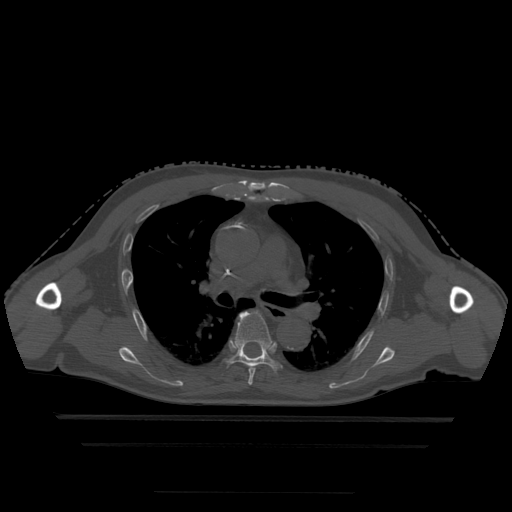
CT including the spine, one axial slice. Slice 321 of 522 in the series (ordered by position). Bone window (W 1800 / L 400 HU). 1.25 mm slice thickness. 512 × 512 image matrix, field of view 436 × 436 mm. Patient age 68 years. From the clinical record (not read from this slice): primary cancer: urothelial.
Annotated regions visible in this slice (semi-automatic segmentation, software-assisted and operator-edited):
- T5 vertebra: bounding box [x1, y1, x2, y2] px = [248, 368, 256, 386]
- T6 vertebra: [225, 312, 283, 372]